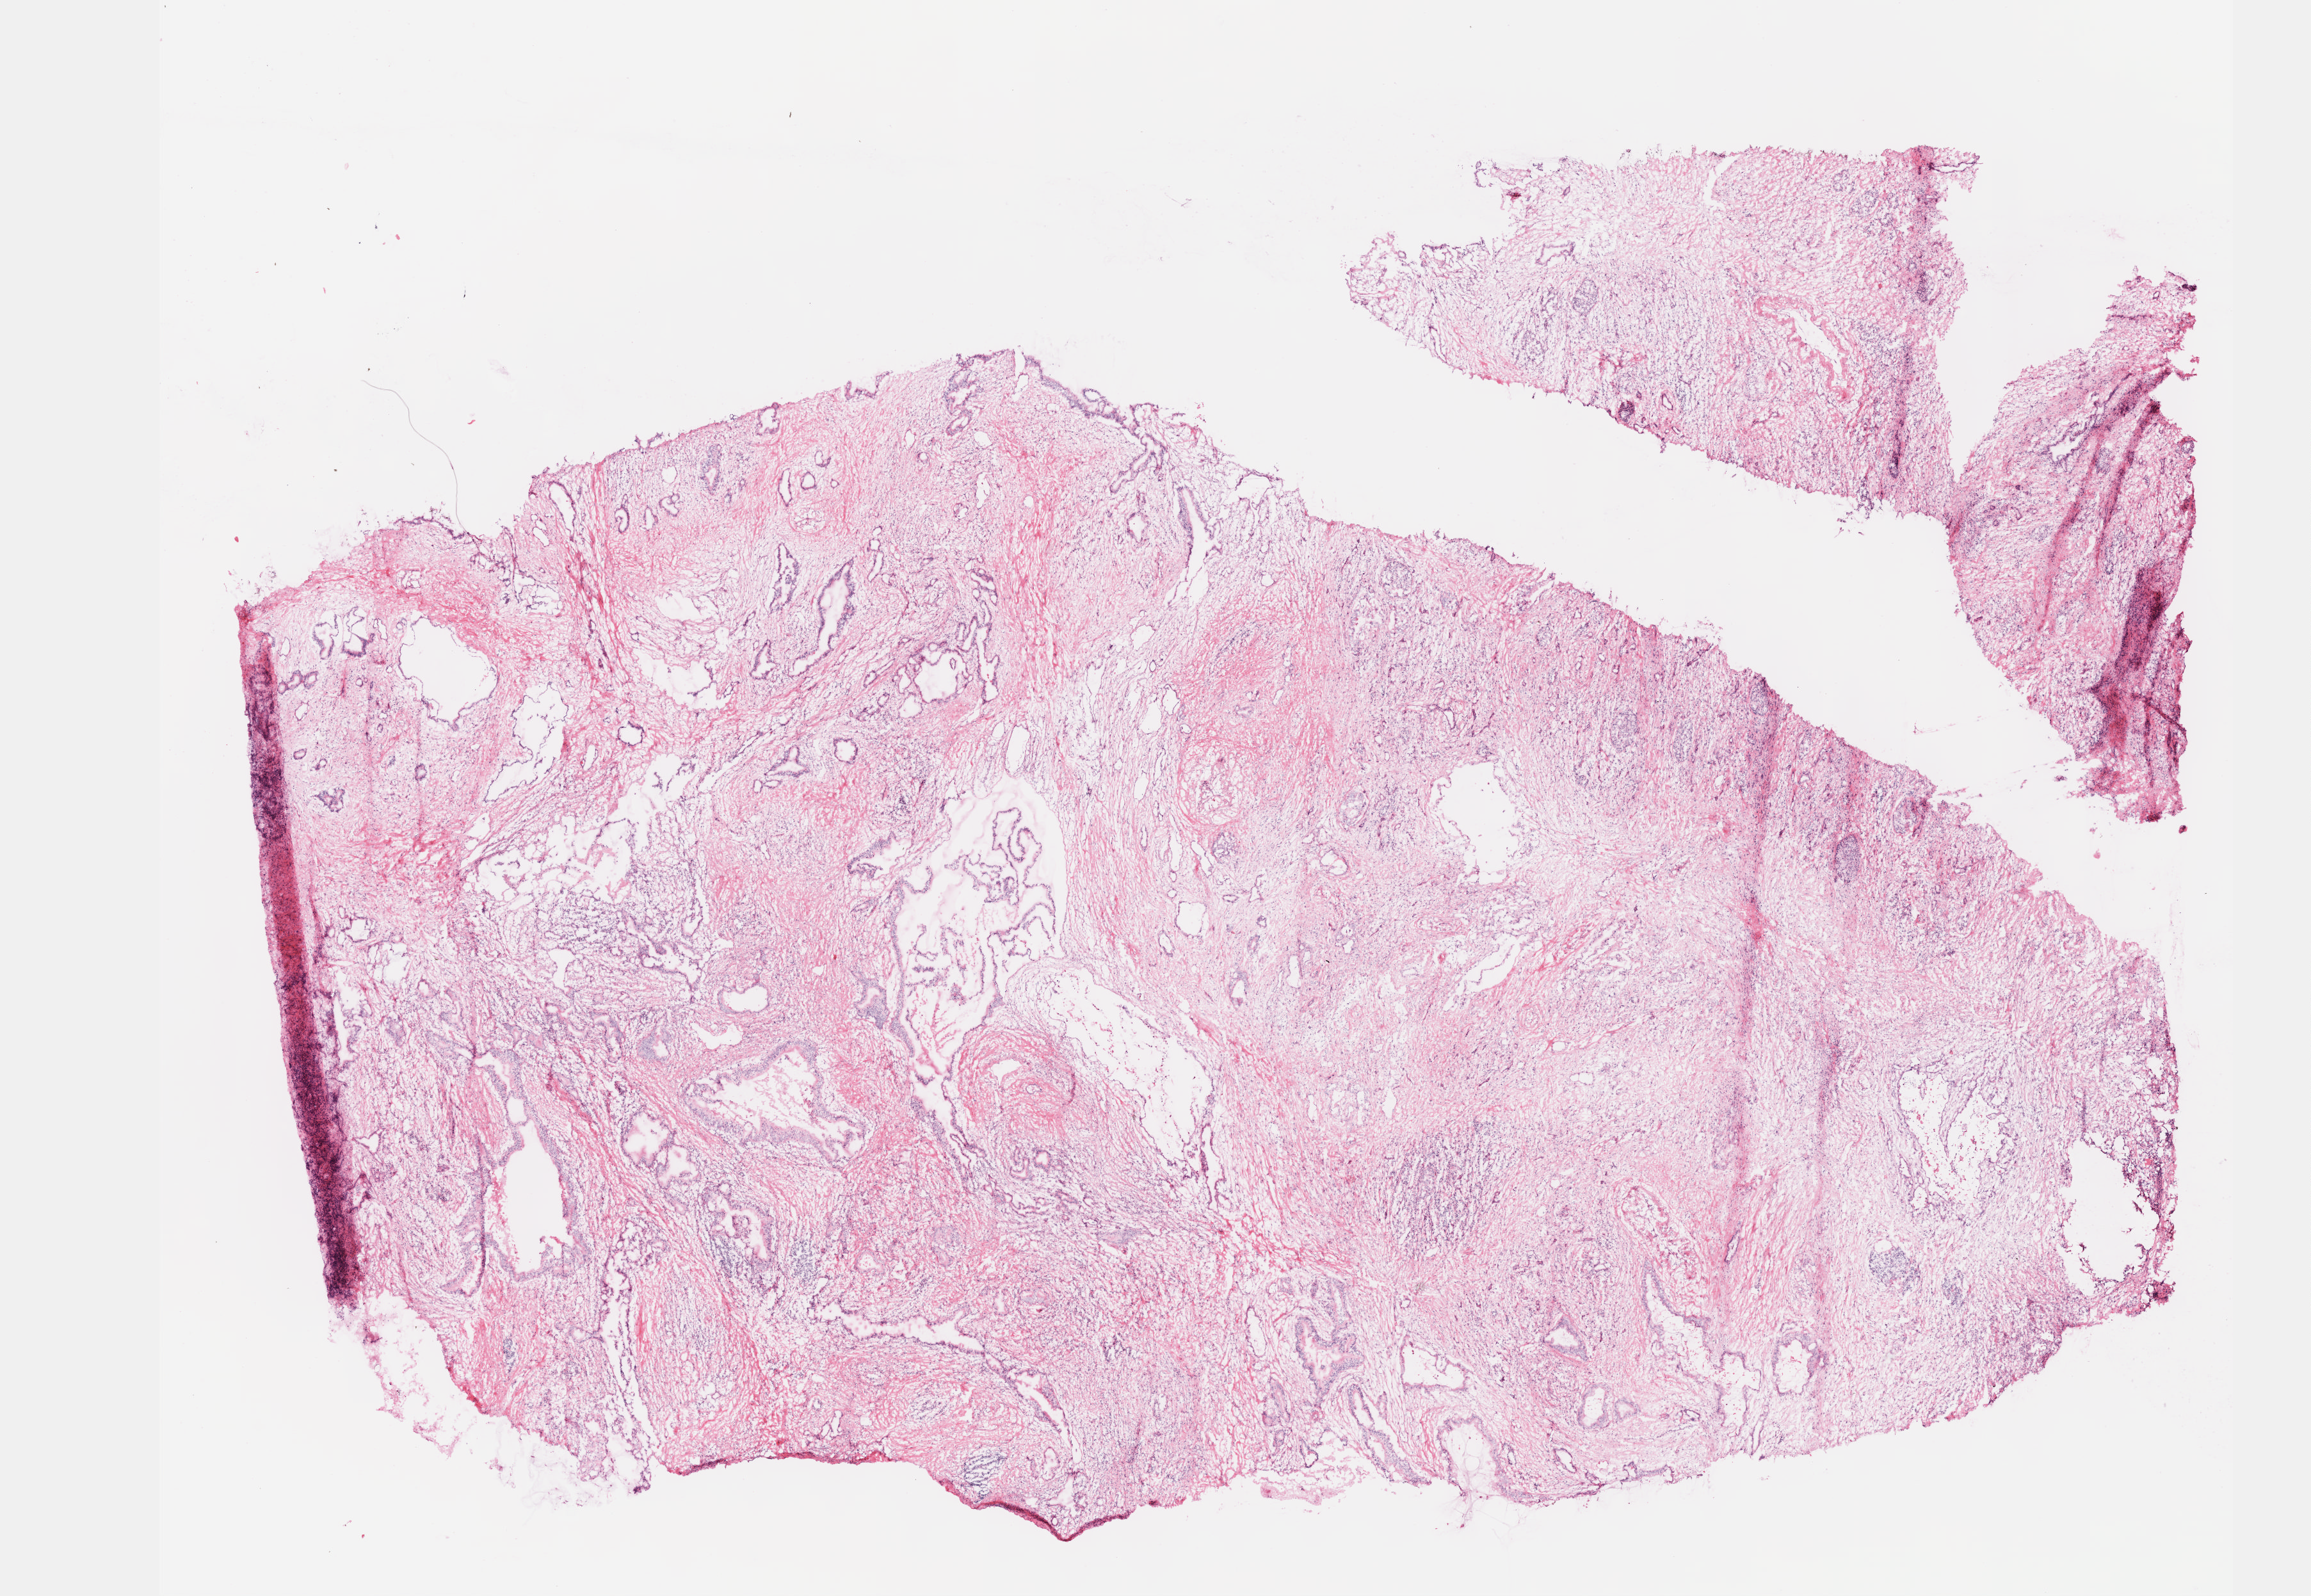
Whole-slide histology image, H&E-stained — shown as a low-resolution overview of the whole scanned area (about 14.6 x 10.1 mm, from a 40x scan), formalin-fixed paraffin-embedded (FFPE) diagnostic section, sample: primary tumour, pancreas. Male patient; age at initial diagnosis 85 years. Histologic grade: G2 (moderately differentiated).
AJCC pathologic stage: IA (7th edition). Lymph nodes positive (case pathology): 0 of 9 examined. TNM: T1 N0 MX. Histologic diagnosis: Infiltrating duct carcinoma, NOS (tail of pancreas).